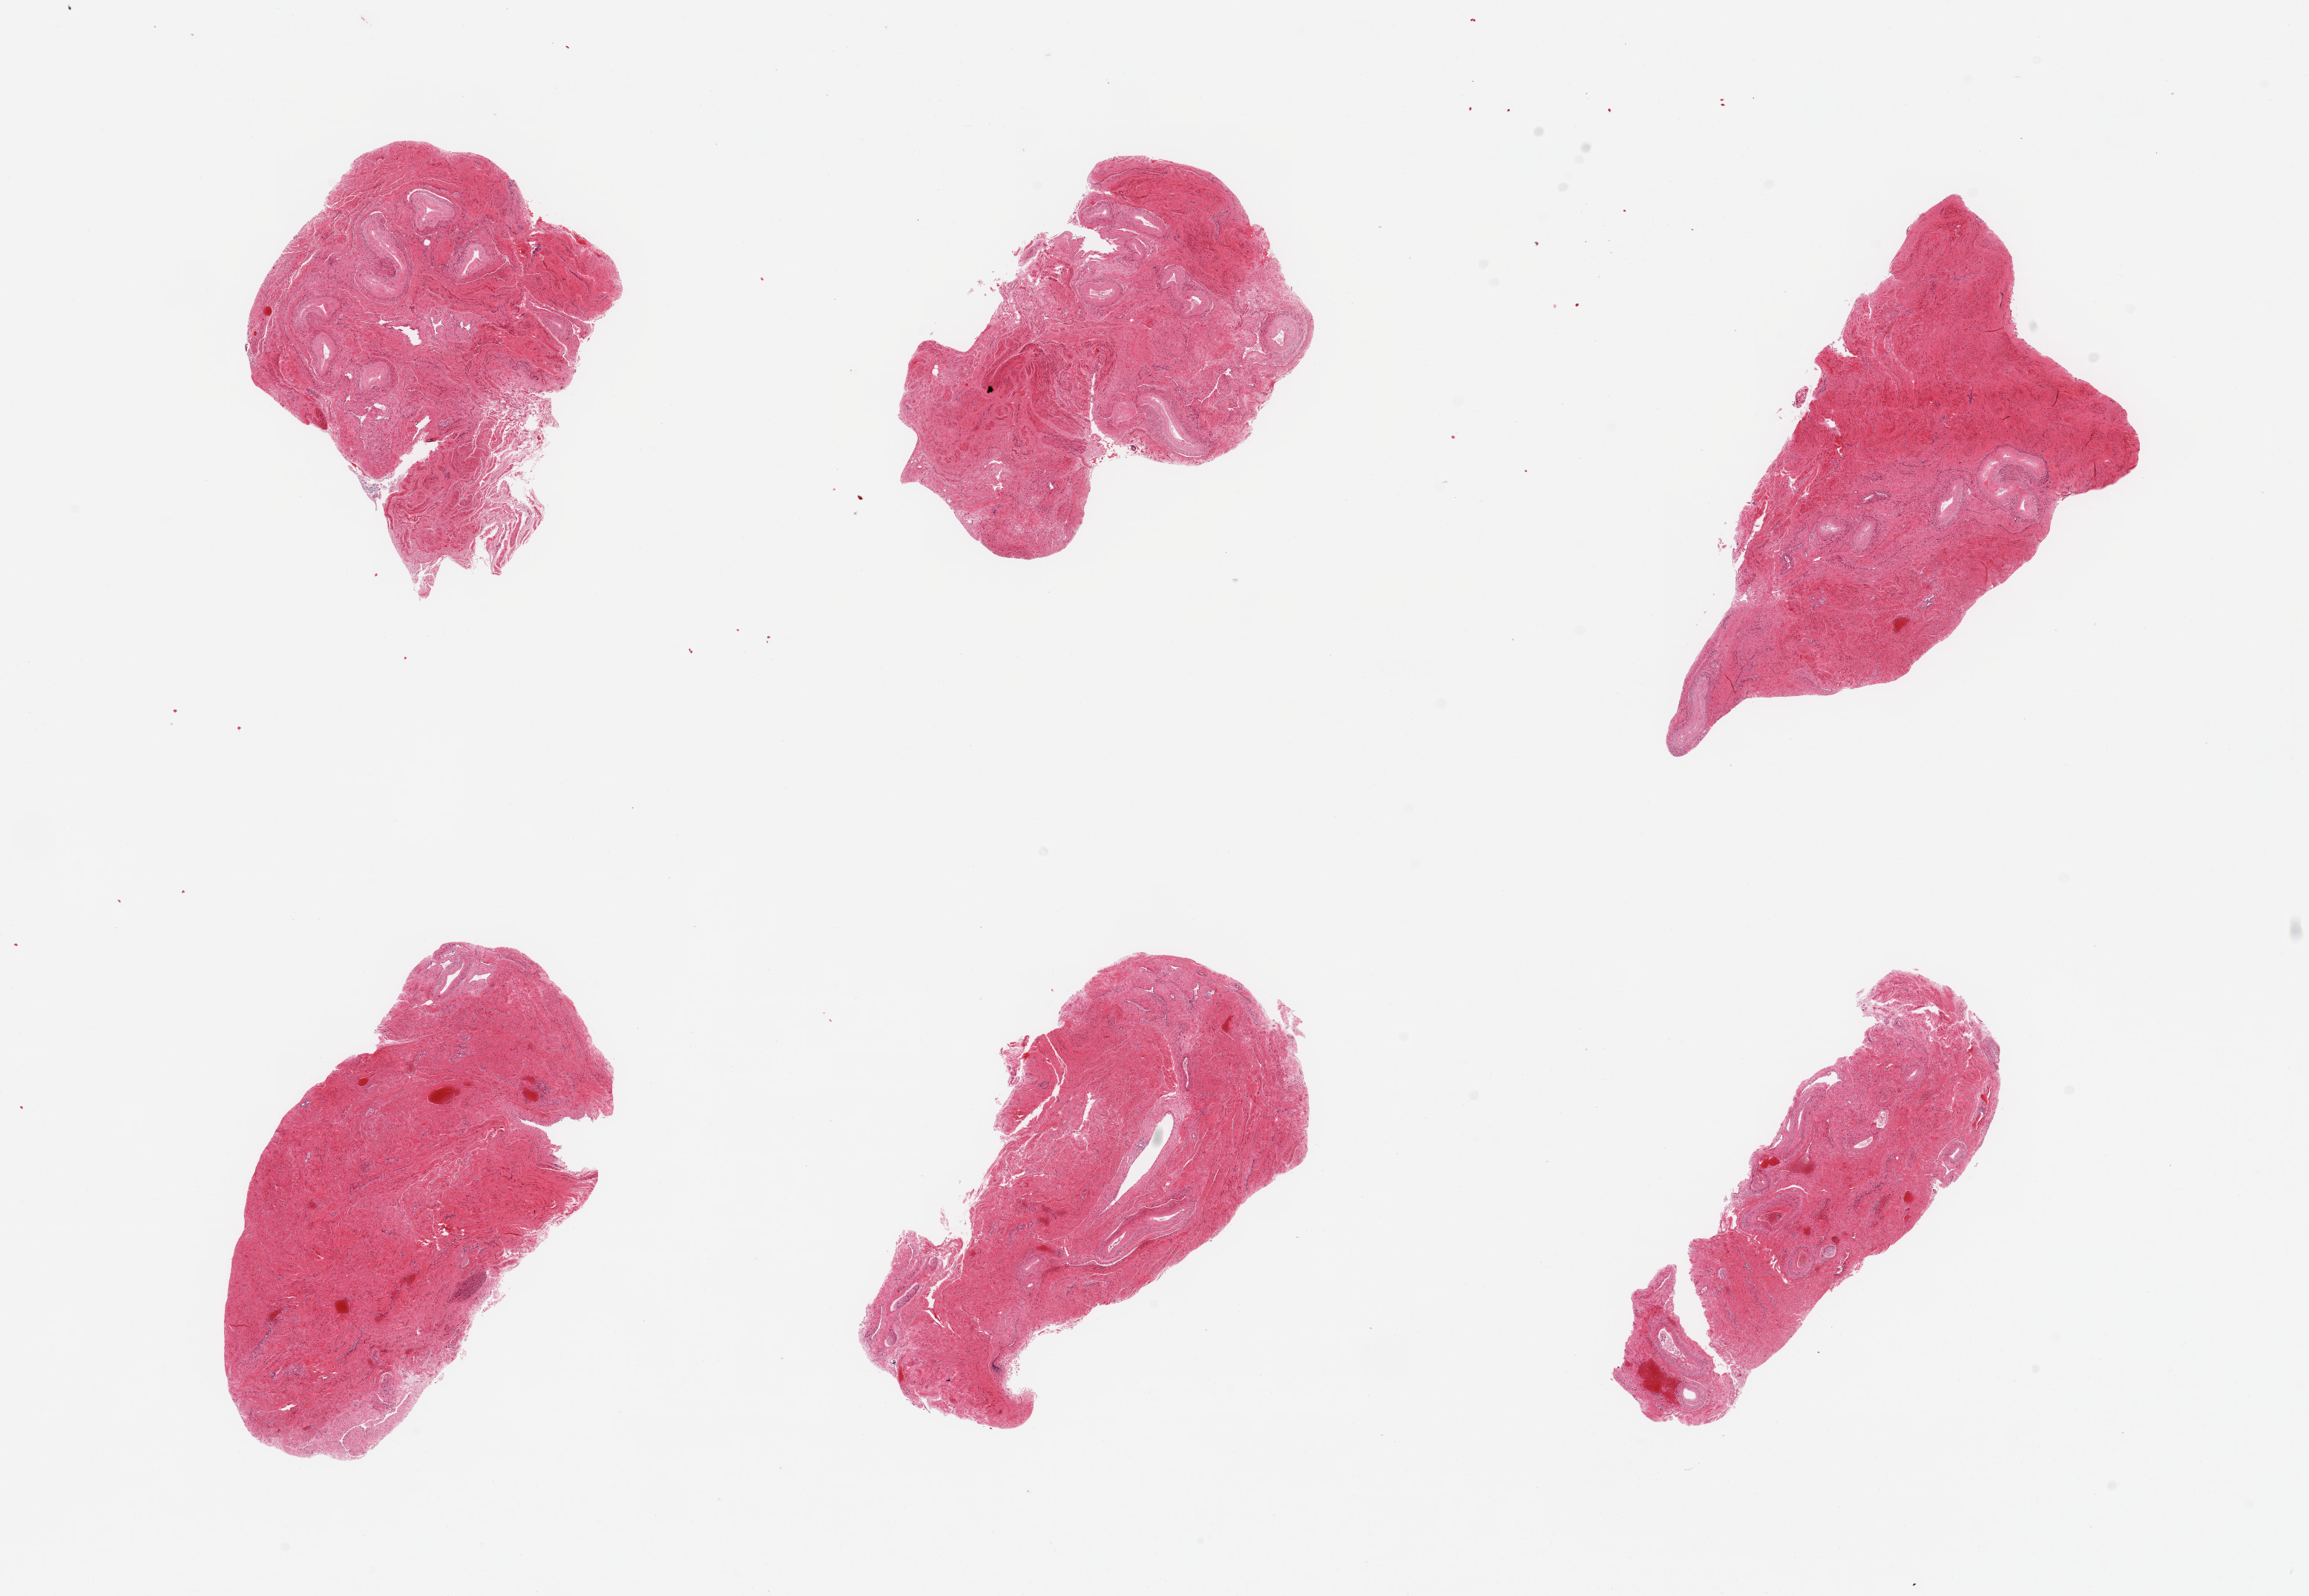
Digitized H&E-stained section, brightfield, whole scanned area (about 24.6 x 17.0 mm, acquisition: 20x scan) shown as a low-resolution overview. PAXgene-fixed paraffin-embedded (PFPE) section. Target tissue: vagina. Tissue donor sample. Donor: female.
Review note (as recorded): 6 pieces; fibrovascular stroma; no sign of vaginal epithelium or wall.